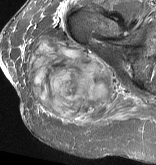
MRI of an extremity soft-tissue mass, one axial slice. Slice 32 of 57 in the series (ordered by position). STIR. MR volume resampled by the dataset authors to the PET/CT grid (not the native acquisition matrix). 3.27 mm slice thickness. 156 × 165 image matrix, field of view 152 × 161 mm. Female patient. From the clinical record (not read from this slice): histological type: epithelioid sarcoma with vascular differentiation; site of the primary tumour: right buttock.
Structures marked on this image (expert contour drawn on MRI and transferred to this co-registered scan by the dataset authors):
- gross tumour volume (mass): bounding box <26,35,114,122> (left, top, right, bottom; pixels)